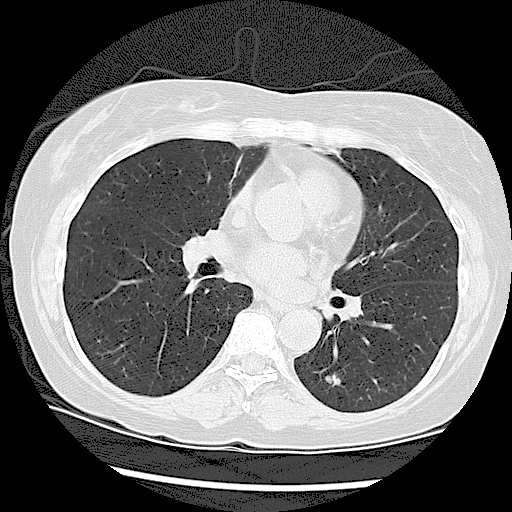
Low-dose screening chest CT, one axial slice. Slice 52 of 108 in the series (ordered by position). Reconstruction kernel LUNG. Lung window (W 1500 / L -600 HU). 2.5 mm slice thickness. 512 × 512 image matrix, field of view 330 × 330 mm.
Annotated regions visible in this slice (expert manual segmentation):
- lesion 1 (tumor, lower lobe of left lung): bounding box [x1, y1, x2, y2] px = [325, 373, 341, 387]